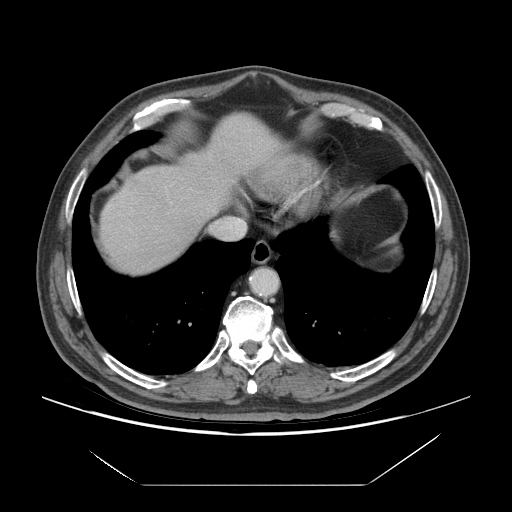
Contrast-enhanced abdominal CT (liver protocol), one axial slice; position 63 of 75 along the scan axis; reconstruction kernel STANDARD; 140 kVp; soft-tissue window (W 400 / L 40 HU); 2.5 mm slice thickness; 512 × 512 image matrix, field of view 420 × 420 mm. From the clinical record (not read from this slice): diagnosis: hepatocellular carcinoma (patient treated with transarterial chemoembolisation; whether this scan precedes or follows treatment is not stated here); TNM stage (as recorded): Stage-I; Child-Pugh class: A; tumour differentiation: well differentiated; tumour nodularity: uninodular.
Outlined on this slice (semi-automatically segmented with operator editing):
- liver parenchyma outside the tumour (the mass and vessels are separate outlines, so this box may not span the whole liver): bounding box [x1, y1, x2, y2] px = [100, 115, 292, 272]